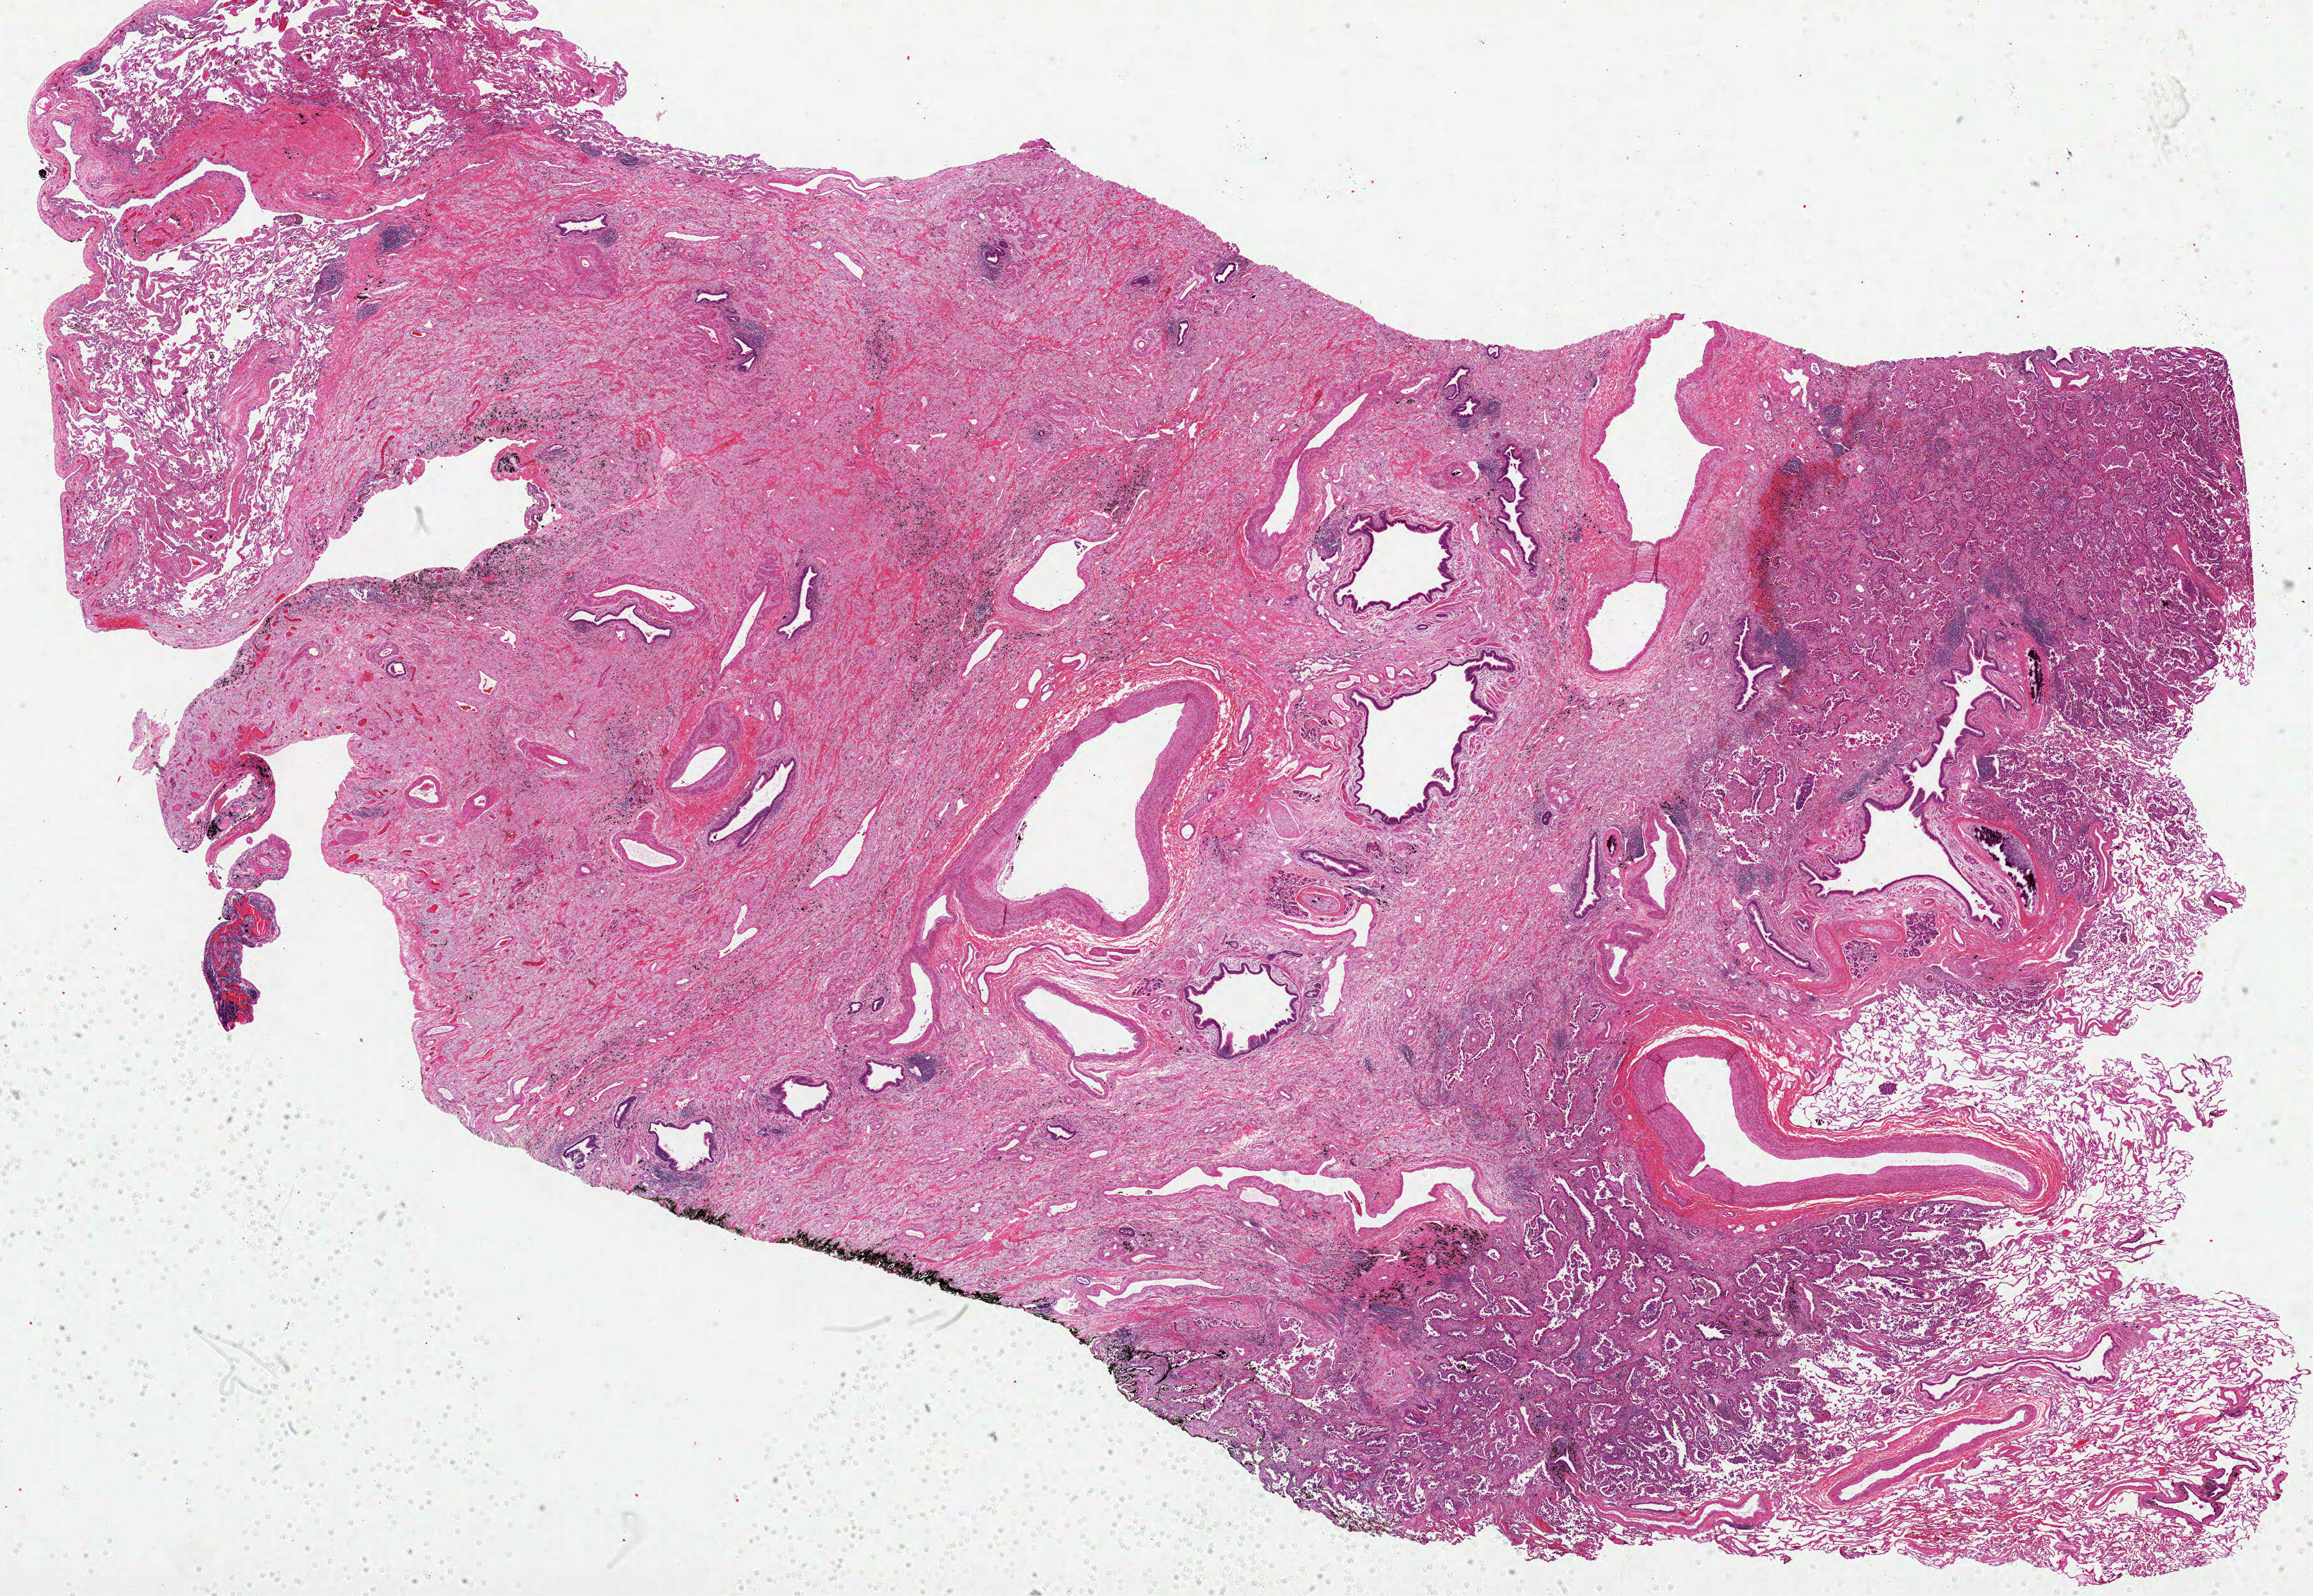
Whole-slide histology image, Hematoxylin and eosin (H&E) stained, shown as a low-resolution overview of the whole scanned area (about 29.0 x 20.0 mm, acquisition: 40x scan), formalin-fixed paraffin-embedded (FFPE) diagnostic section, lung, primary tumour sample. Female patient; age at initial diagnosis 61 years.
AJCC pathologic stage: IIB. Laterality: right. Diagnosis: Adenocarcinoma, NOS (lower lobe, lung).